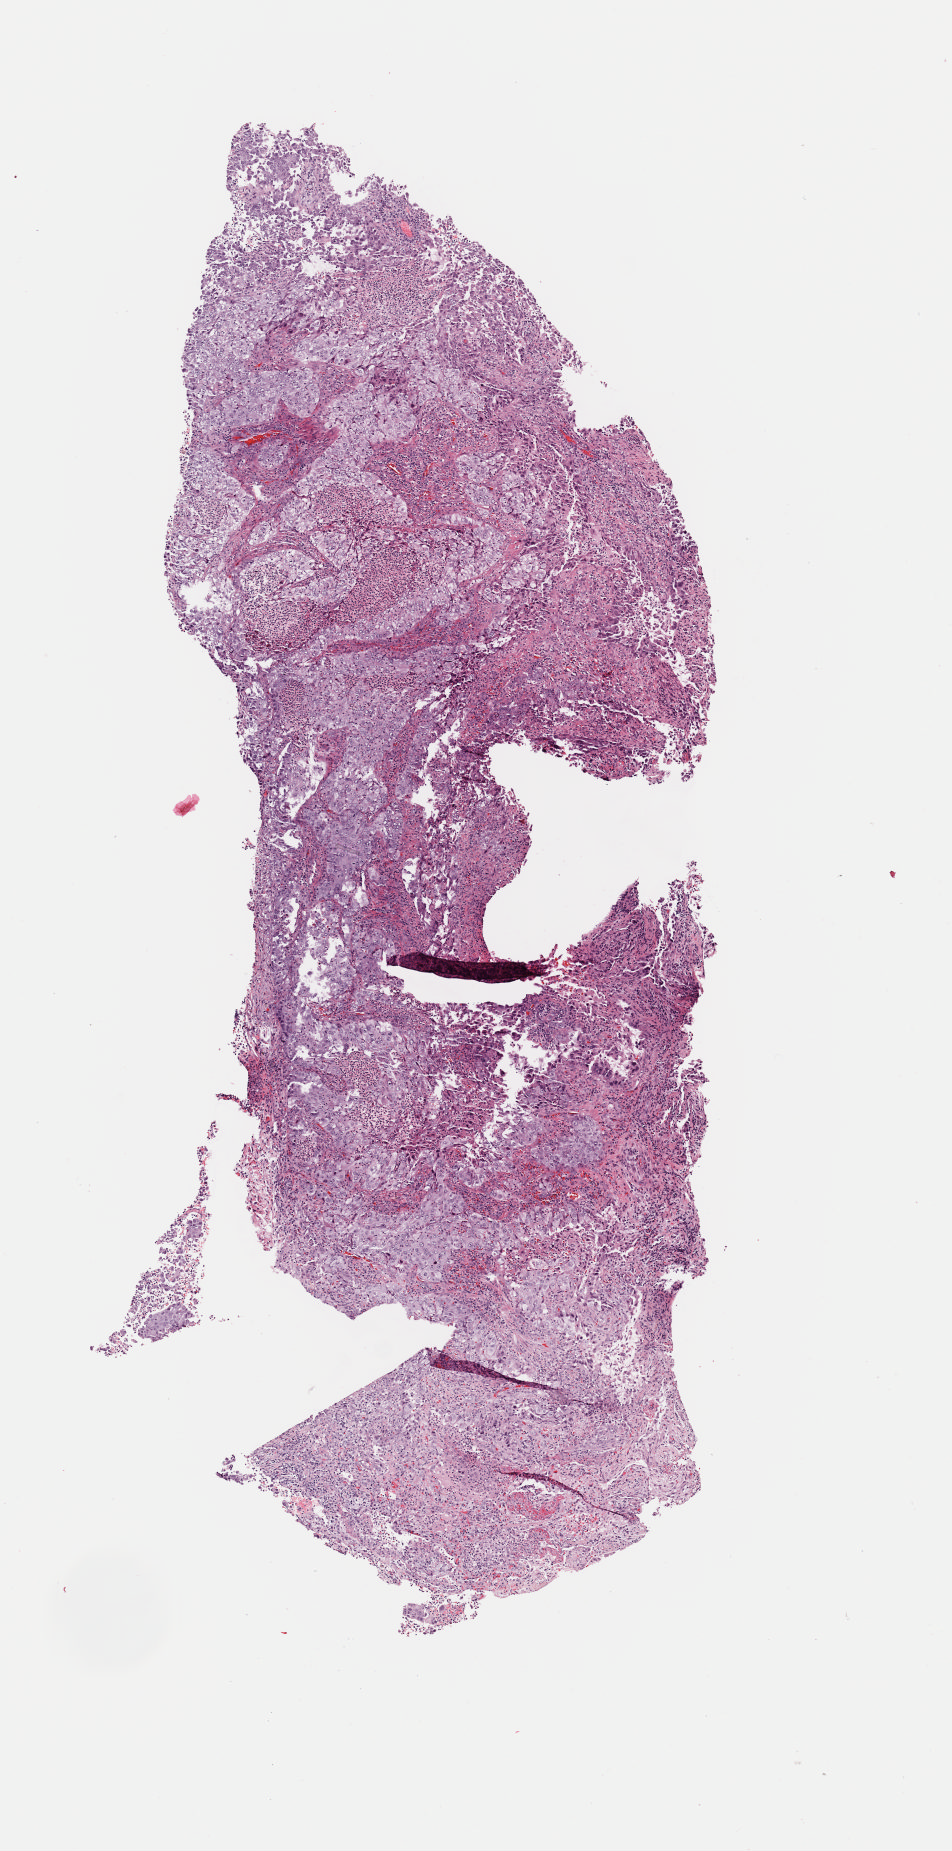
H&E whole-slide image, low-resolution overview of the scanned area, about 3.8 x 7.3 mm (slide scanned at 40x). Frozen section from the bottom of the tissue portion. Lung, primary tumour sample. Male, age 51 years at initial diagnosis. Composition of this section per pathologist review: tumour cells 60%, tumour nuclei 70%, normal cells 0%, stromal cells 30%, necrosis 10%. Inflammatory infiltration, as recorded: lymphocyte infiltration 0%, monocyte infiltration 0%, neutrophil infiltration 0%.
* pathologic diagnosis: Adenocarcinoma, NOS (upper lobe, lung)
* AJCC pathologic stage: IB (6th edition)
* TNM: T2 N0 M0